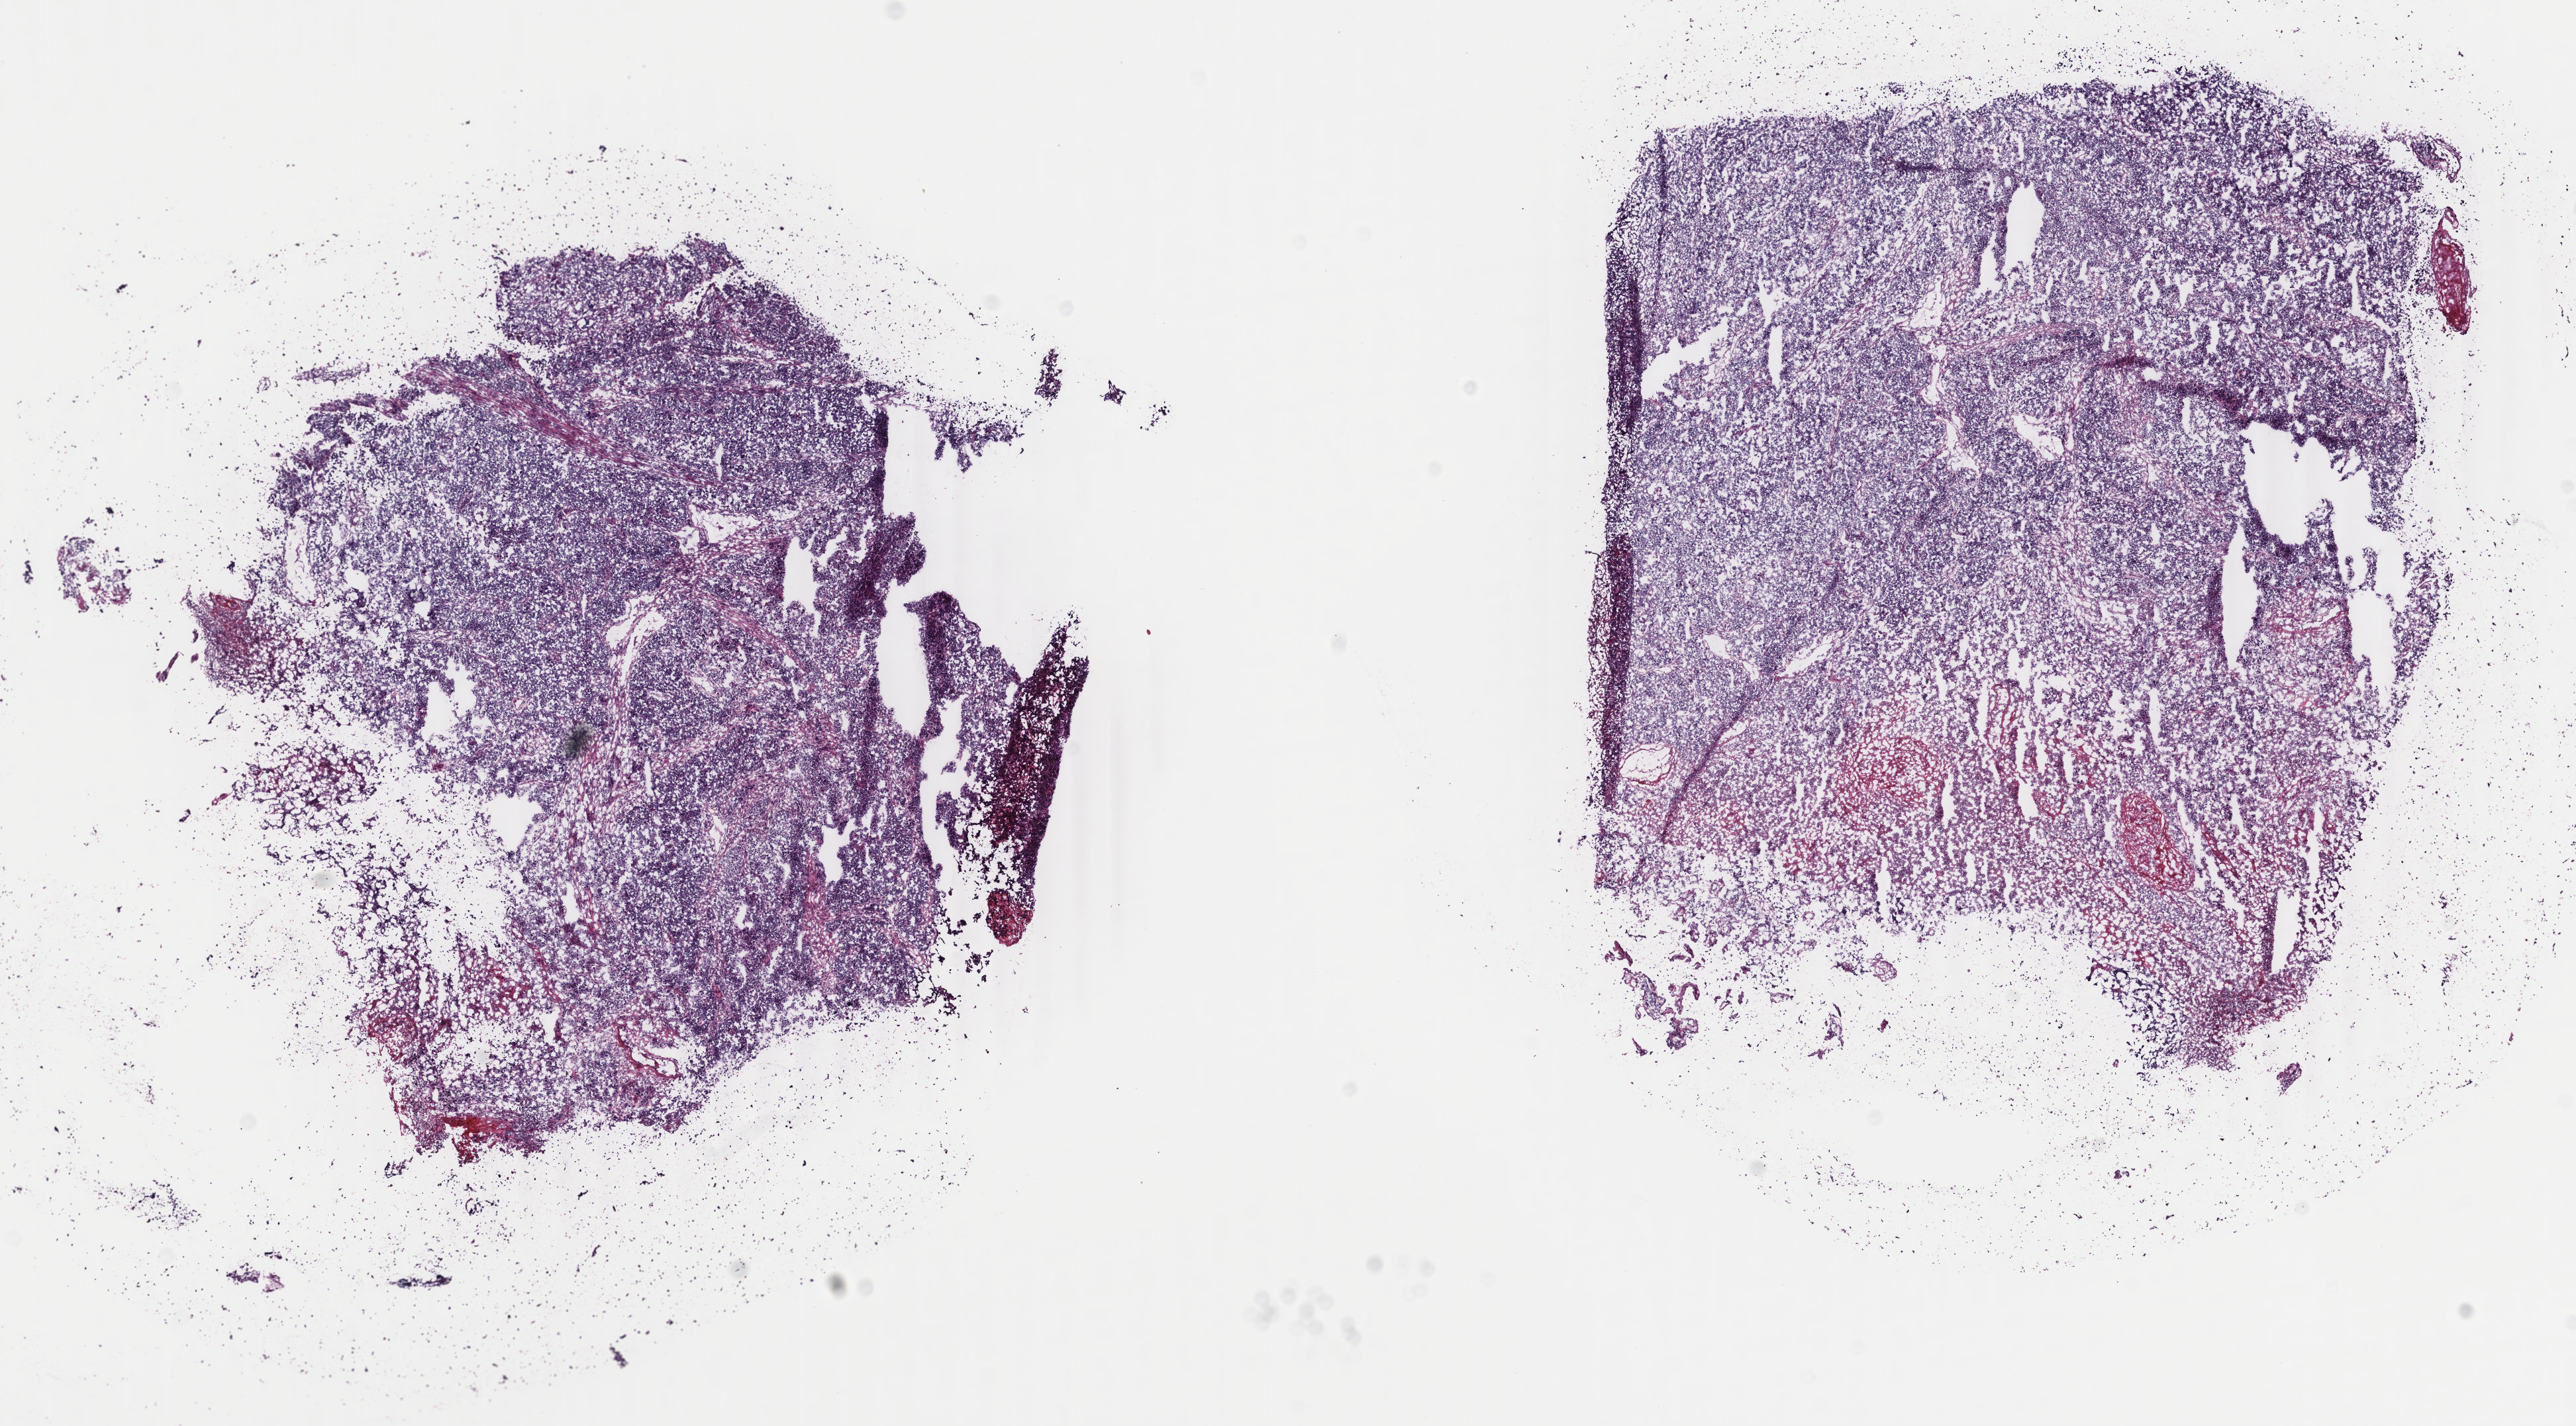
Whole-slide histology image, Hematoxylin and eosin (H&E) stained, low-resolution overview of the scanned area, about 15.5 x 8.6 mm (acquisition: 40x scan), frozen section from the top of the tissue portion, uterus, primary tumour sample. Patient: female, age at initial diagnosis 55 years. Histologic grade: G3 (poorly differentiated). Composition of this section per pathologist review: tumour cells 70%, tumour nuclei 90%, normal cells 0%, stromal cells 10%, necrosis 20%. Inflammatory infiltration, as recorded: lymphocyte infiltration 40%, monocyte infiltration 0%, neutrophil infiltration 57%.
Lymph nodes positive (case pathology): 1 of 8 examined. FIGO stage: IIIC. Histologic diagnosis: Endometrioid adenocarcinoma, NOS.